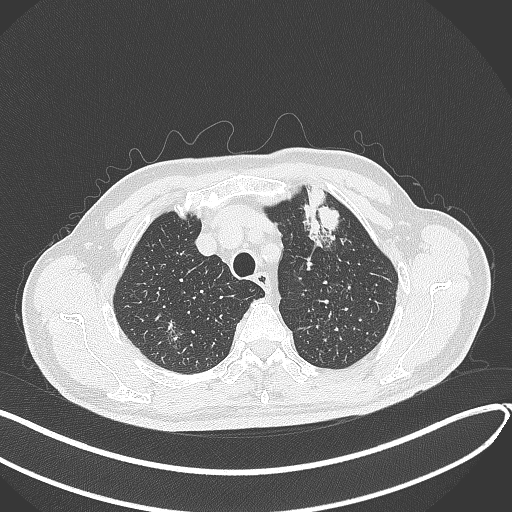
Chest CT, one axial slice; slice 346 of 459 in the series (ordered by position); reconstruction kernel B70f; 120 kVp; lung window (W 1500 / L -600 HU); 512 × 512 image matrix. Male patient, age 74 years. Case-level facts recorded for this patient, not image findings: clinical TNM (as recorded): T2b N0 M1c.
Outlined on this slice (rectangle marked by the reading radiologist):
- lung tumour (recorded histology: adenocarcinoma): box from (x=296, y=182) to (x=347, y=253) px